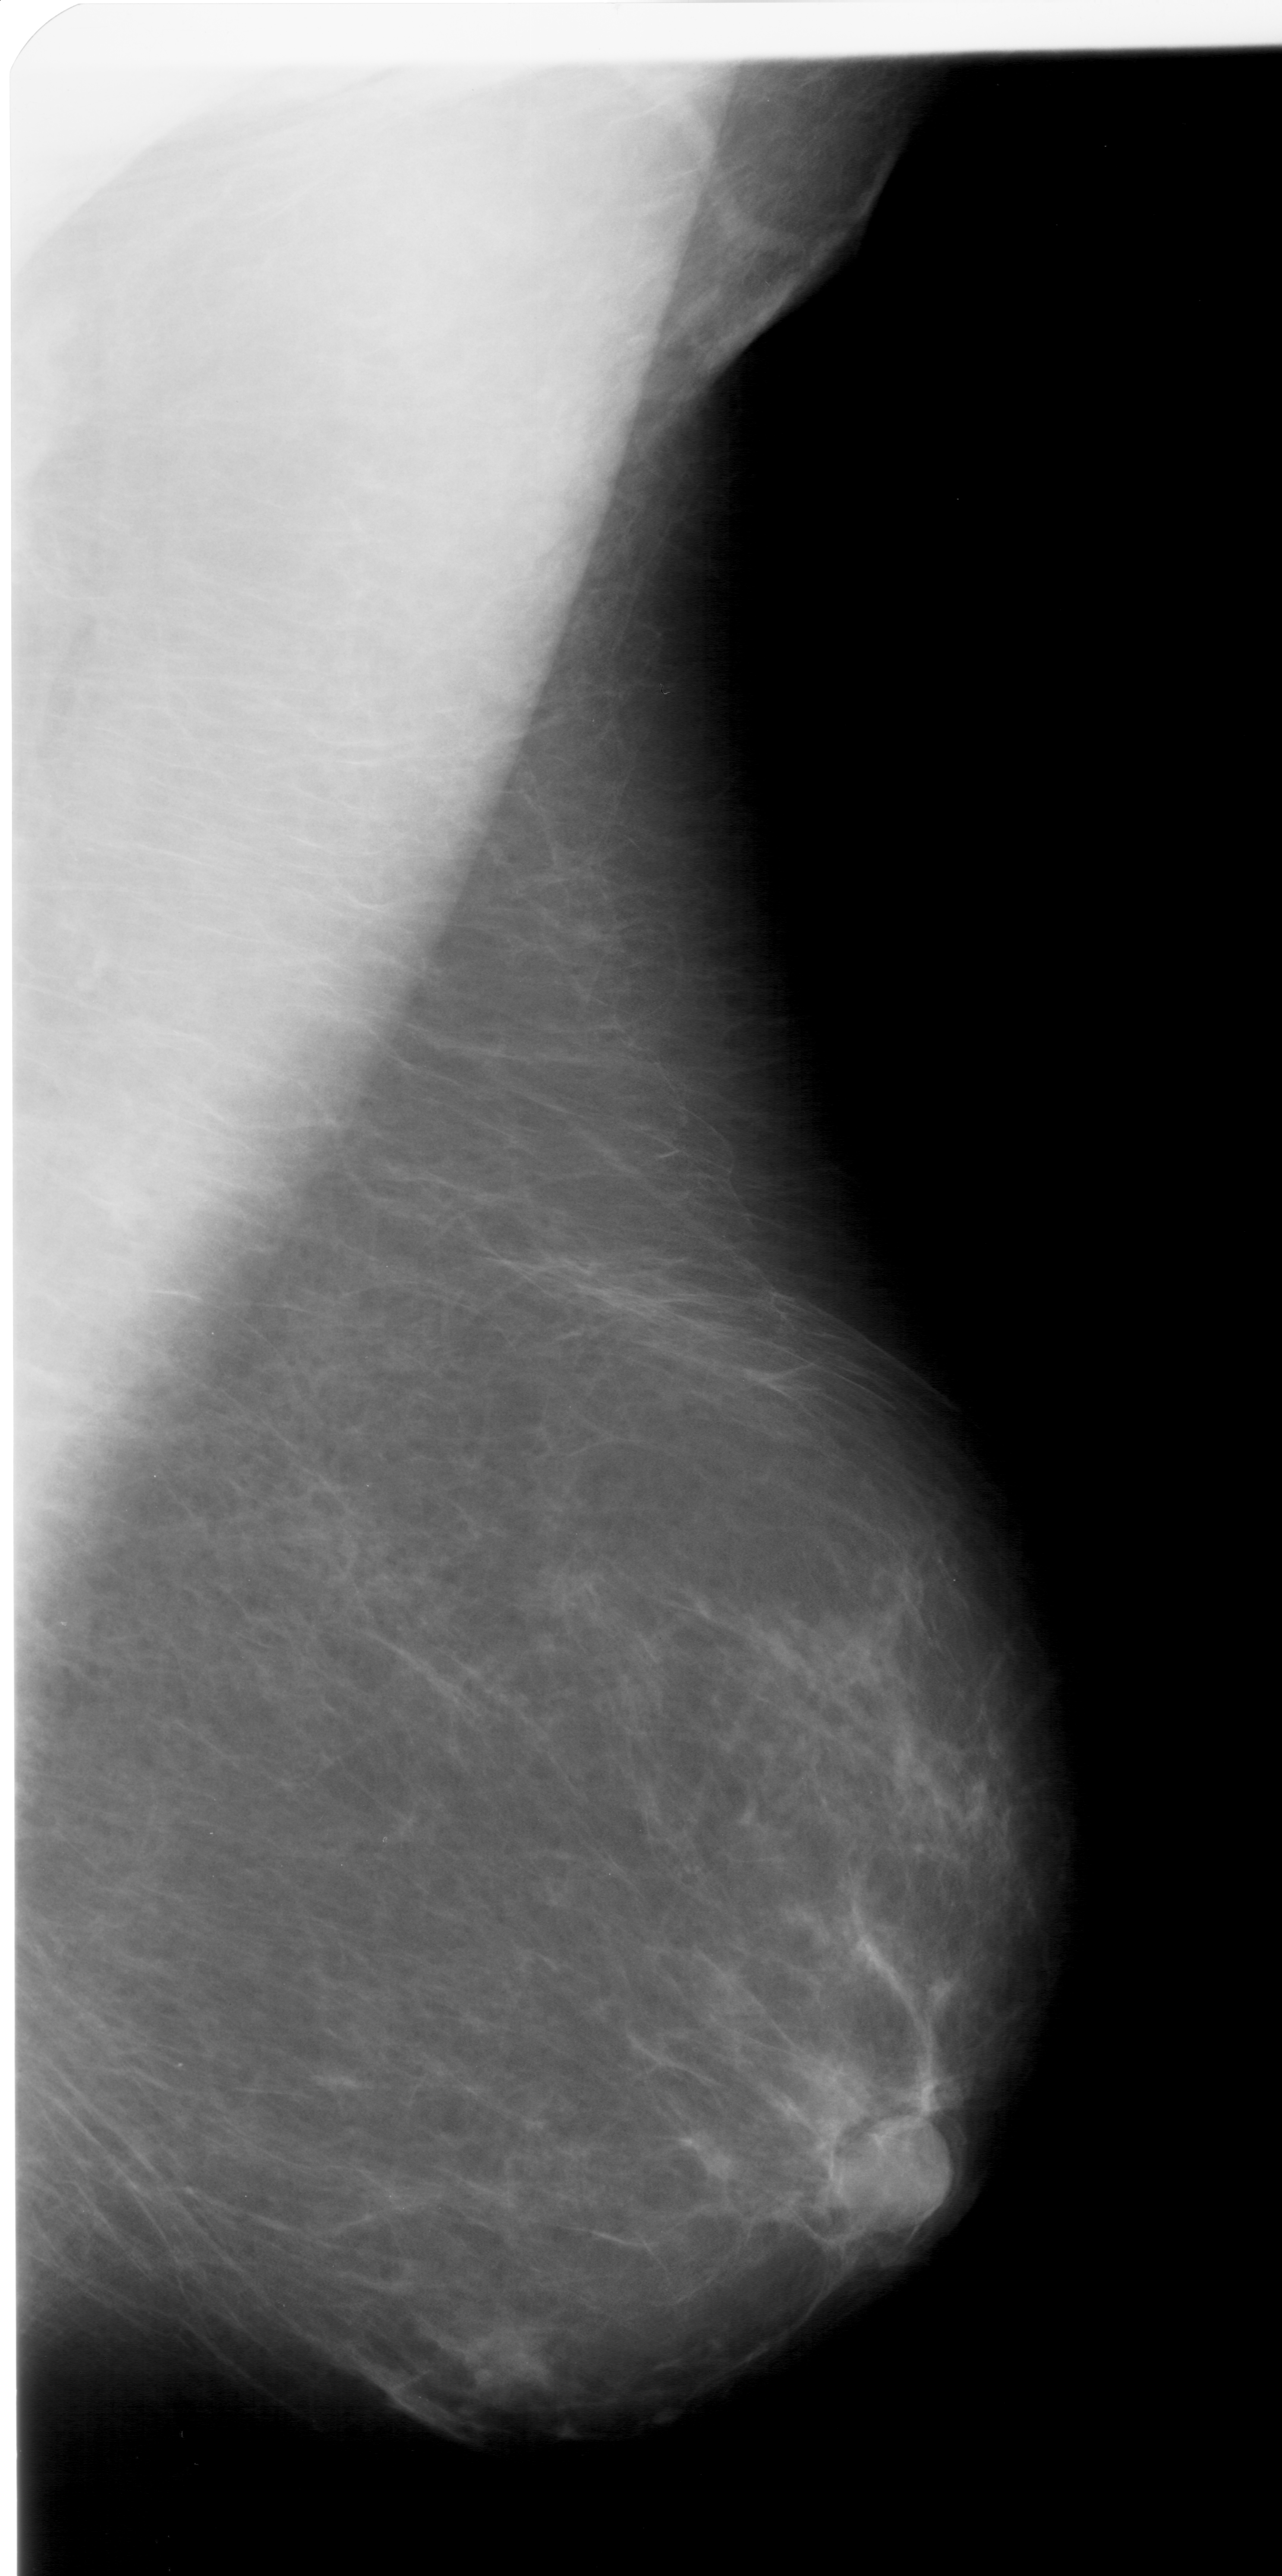
Scanned film-screen mammogram; right breast; mediolateral oblique (MLO) view; breast composition: scattered fibroglandular densities (BI-RADS density category 2 of 4); 1282 × 2576 image matrix.
Marked abnormalities (boxes around the expert regions of interest):
- mass, shape irregular, margins ill defined; BI-RADS assessment category 4; subtlety rating 1 on a 1 (subtle) to 5 (obvious) scale; pathology (as recorded): benign: box from (x=432, y=2310) to (x=555, y=2406) px